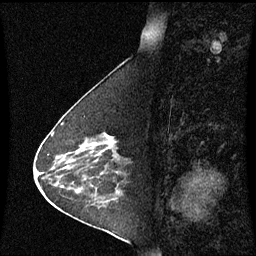
Breast MRI (dynamic contrast-enhanced), one sagittal slice. Slice 25 of 60 in the series (ordered by position). Dynamic contrast-enhanced series, image 2 of 3 at this slice position (ordered by acquisition). 1.5 T. TE 4.2 ms, TR 8.9 ms. 256 × 256 image matrix. Patient: female, 63 years. Case-level facts recorded for this patient, not image findings: setting: breast cancer imaged before/during neoadjuvant chemotherapy; receptor status: HR-positive, HER2-negative.
Structures marked on this image (semi-automatic segmentation, software-assisted and operator-edited):
- analysis volume of interest (the breast-tissue region the enhancement analysis was run in; not a lesion): bounding box <76,134,123,178> (left, top, right, bottom; pixels)
- tumour enhancement mask (voxels above the 70 % enhancement threshold inside the analysis volume of interest): <105,134,115,146>